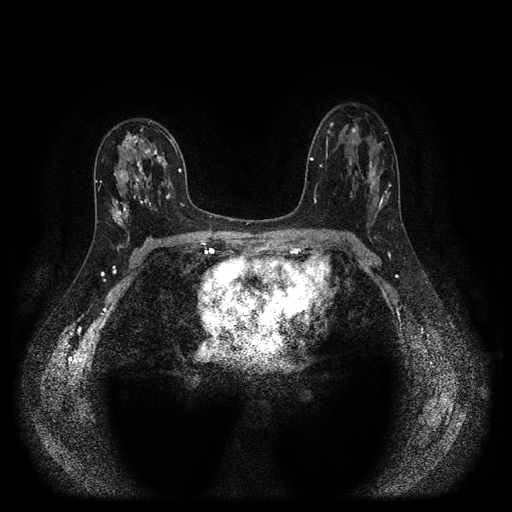
Breast MRI (dynamic contrast-enhanced, multi-phase), one axial slice. Position 62 of 116 along the scan axis. Dynamic contrast-enhanced series, time point 2 of 5 at this slice position (early post-contrast). 1.5 T. TE 2.7 ms, TR 5.4 ms. 512 × 512 image matrix, field of view 330 × 330 mm. Female patient, age 47 years.
Outlined on this slice (semi-automatic segmentation, software-assisted and operator-edited):
- breast lesion (labelled 'tumour' in the annotation; benign lesions carry a separate 'benign' label): bounding box [x1, y1, x2, y2] px = [113, 133, 174, 221]